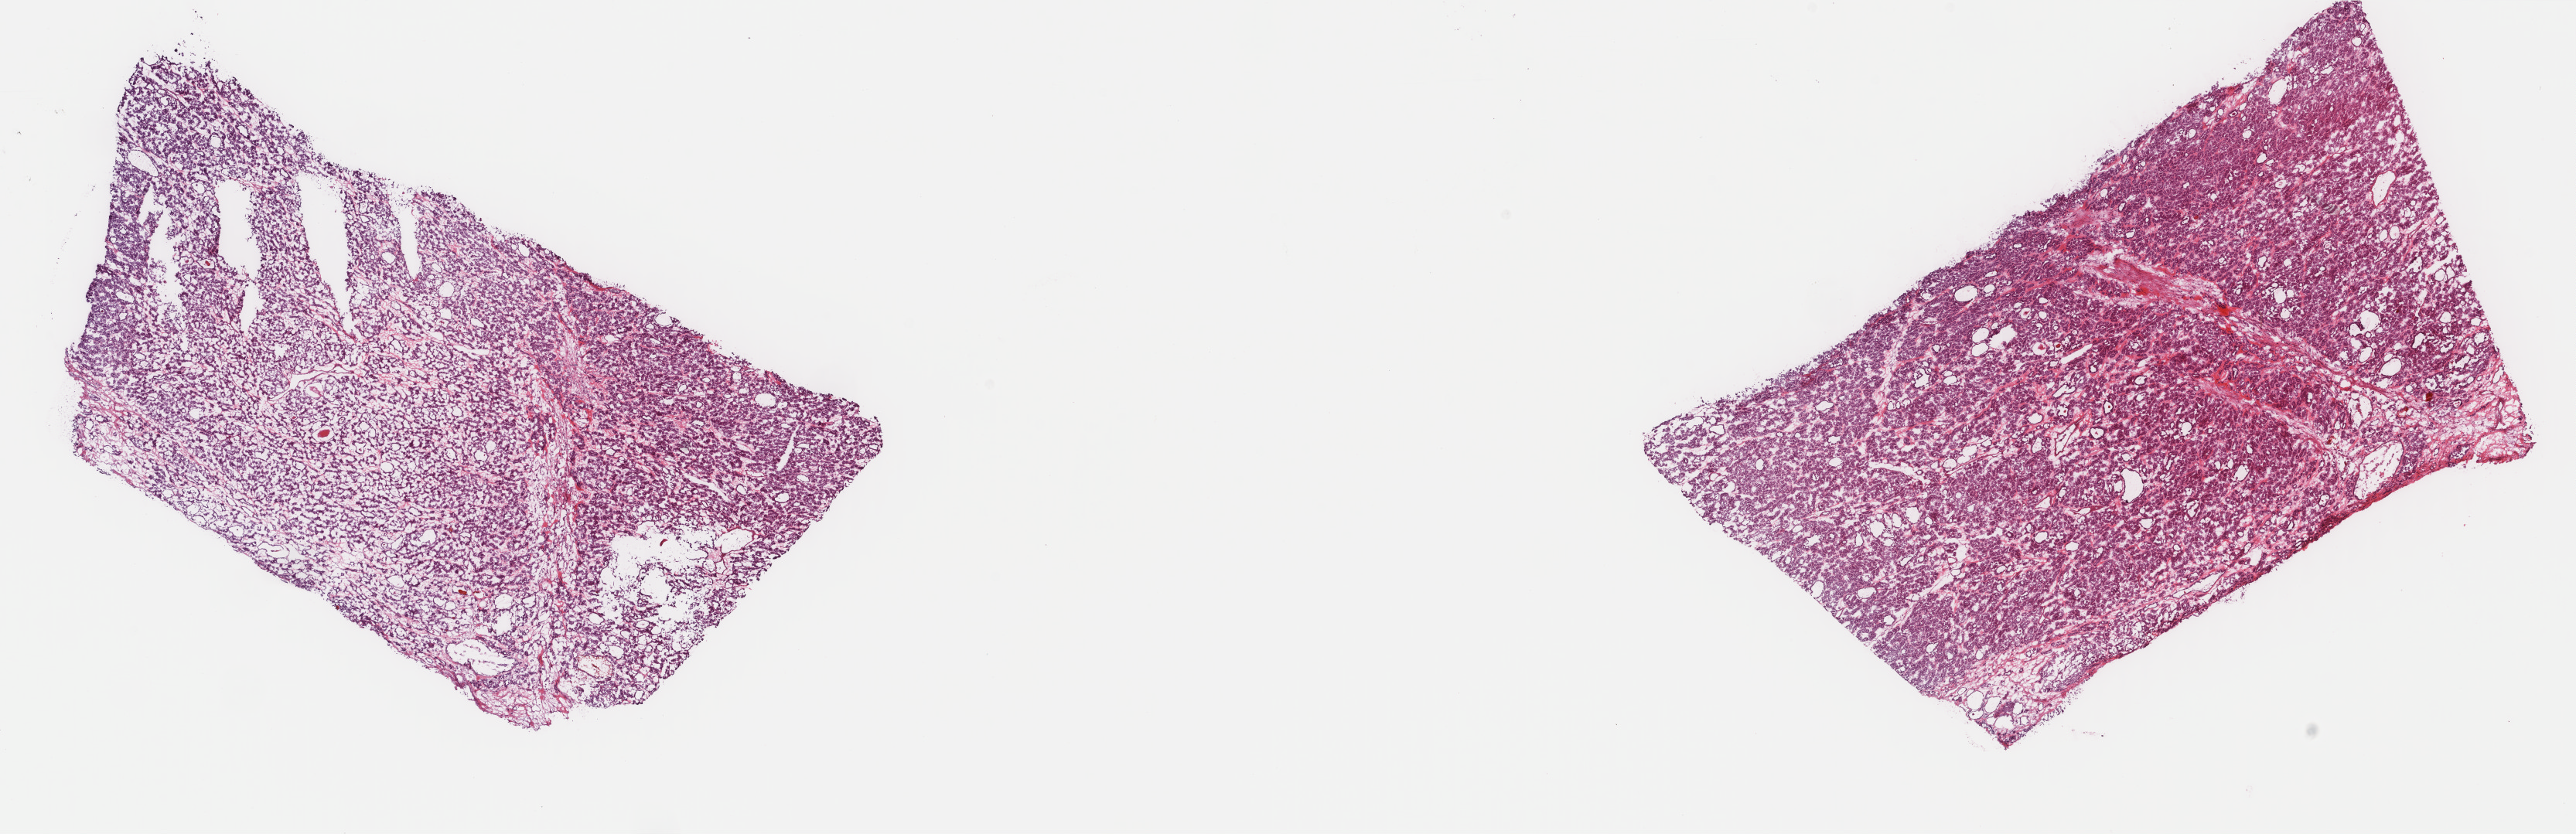
Digitized H&E-stained tissue section (whole slide) — shown as a low-resolution overview of the whole scanned area (about 26.4 x 8.6 mm, acquisition: 40x scan). Frozen section. Thyroid, primary tumour sample. Female, age 29 years at initial diagnosis. Pathologist review of this section (percent, as recorded): tumour cells 85%, tumour nuclei 85%, normal cells 0%, stromal cells 15%, necrosis 0%. Infiltration values recorded for this section: lymphocyte infiltration 0%, monocyte infiltration 0%, neutrophil infiltration 0%.
Histologic diagnosis: Papillary adenocarcinoma, NOS (thyroid gland). AJCC pathologic stage: I (7th edition).